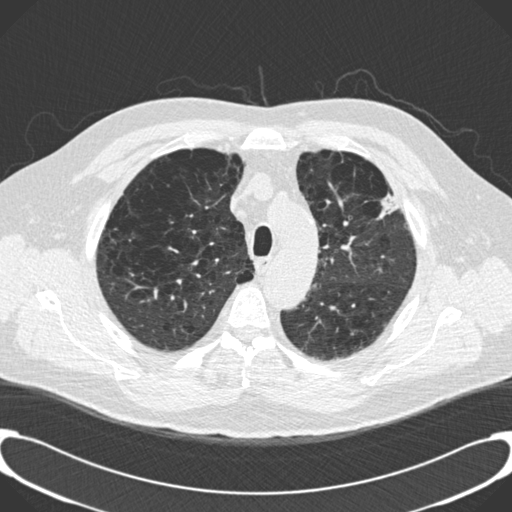
Axial slice from a low-dose chest CT screening exam, third screening round (two years after baseline), lung window (W 1500 / L -600 HU), 2 mm slice thickness, standard (soft-tissue) reconstruction kernel (B30f), slice 38 of 189 in the series. Male, age 59 years at enrolment. Current smoker at enrolment.
Expert-annotated lung lesion, bounding box <362,169,412,227> (left, top, right, bottom; pixels). Screening reader's record for this exam: no non-calcified nodule ≥4 mm recorded. Participant outcome: lung cancer diagnosed 134 days after this screen — bronchiolo-alveolar carcinoma, mixed mucinous and non-mucinous, left upper lobe, stage IA (AJCC 6th edition), 20 mm at pathology.